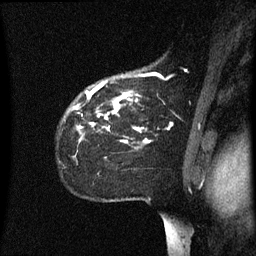
Breast MRI (dynamic contrast-enhanced), one sagittal slice; slice 46 of 60 in the series (ordered by position); dynamic contrast-enhanced series, image 2 of 3 at this slice position (ordered by acquisition); 1.5 T; TE 4.2 ms, TR 8.4 ms; 2.2 mm slice thickness; 256 × 256 image matrix. Female patient, age 35 years. Case-level facts recorded for this patient, not image findings: setting: breast cancer imaged before/during neoadjuvant chemotherapy; receptor status: HER2-positive.
Outlined on this slice (semi-automatic segmentation, software-assisted and operator-edited):
- analysis volume of interest (the breast-tissue region the enhancement analysis was run in; not a lesion): box from (x=64, y=78) to (x=173, y=163) px
- tumour enhancement mask (voxels above the 70 % enhancement threshold inside the analysis volume of interest): (x=79, y=94)–(x=150, y=143)